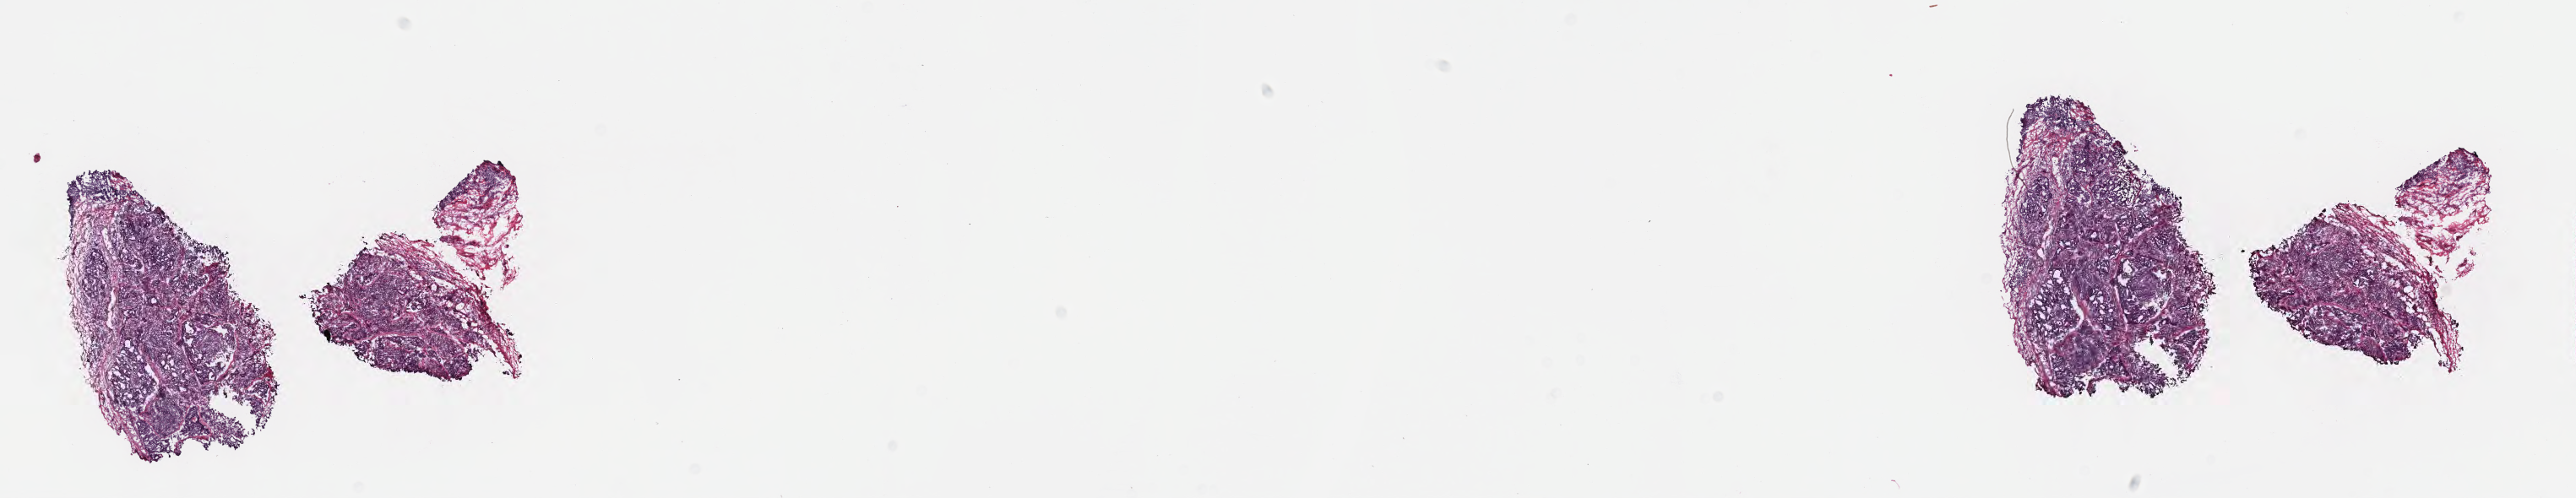
H&E whole-slide image, low-resolution overview of the scanned area, about 24.6 x 4.8 mm. Frozen section. Specimen: metastatic tumor tissue, resected from lymph nodes of axilla or arm. Female patient; age at initial diagnosis 83 years.
Patient diagnosis (primary): Infiltrating duct carcinoma, NOS.